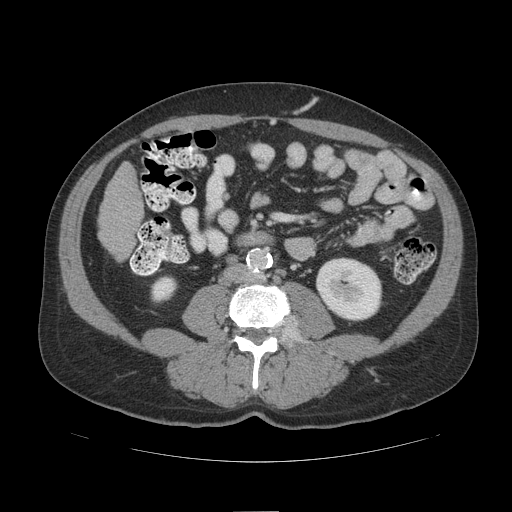
Contrast-enhanced abdominal CT (liver protocol), one axial slice; slice 26 of 109 in the series (ordered by position); soft-tissue window (W 400 / L 40 HU); 2.5 mm slice thickness; 512 × 512 image matrix, field of view 420 × 420 mm. Case-level facts recorded for this patient, not image findings: diagnosis: hepatocellular carcinoma (patient treated with transarterial chemoembolisation; whether this scan precedes or follows treatment is not stated here); TNM stage (as recorded): Stage-IIIB; Child-Pugh class: A; tumour differentiation: poorly differentiated; tumour nodularity: multinodular.
Structures marked on this image (semi-automatic segmentation, software-assisted and operator-edited):
- liver parenchyma outside the tumour (the mass and vessels are separate outlines, so this box may not span the whole liver): bounding box [x1, y1, x2, y2] px = [98, 162, 142, 258]